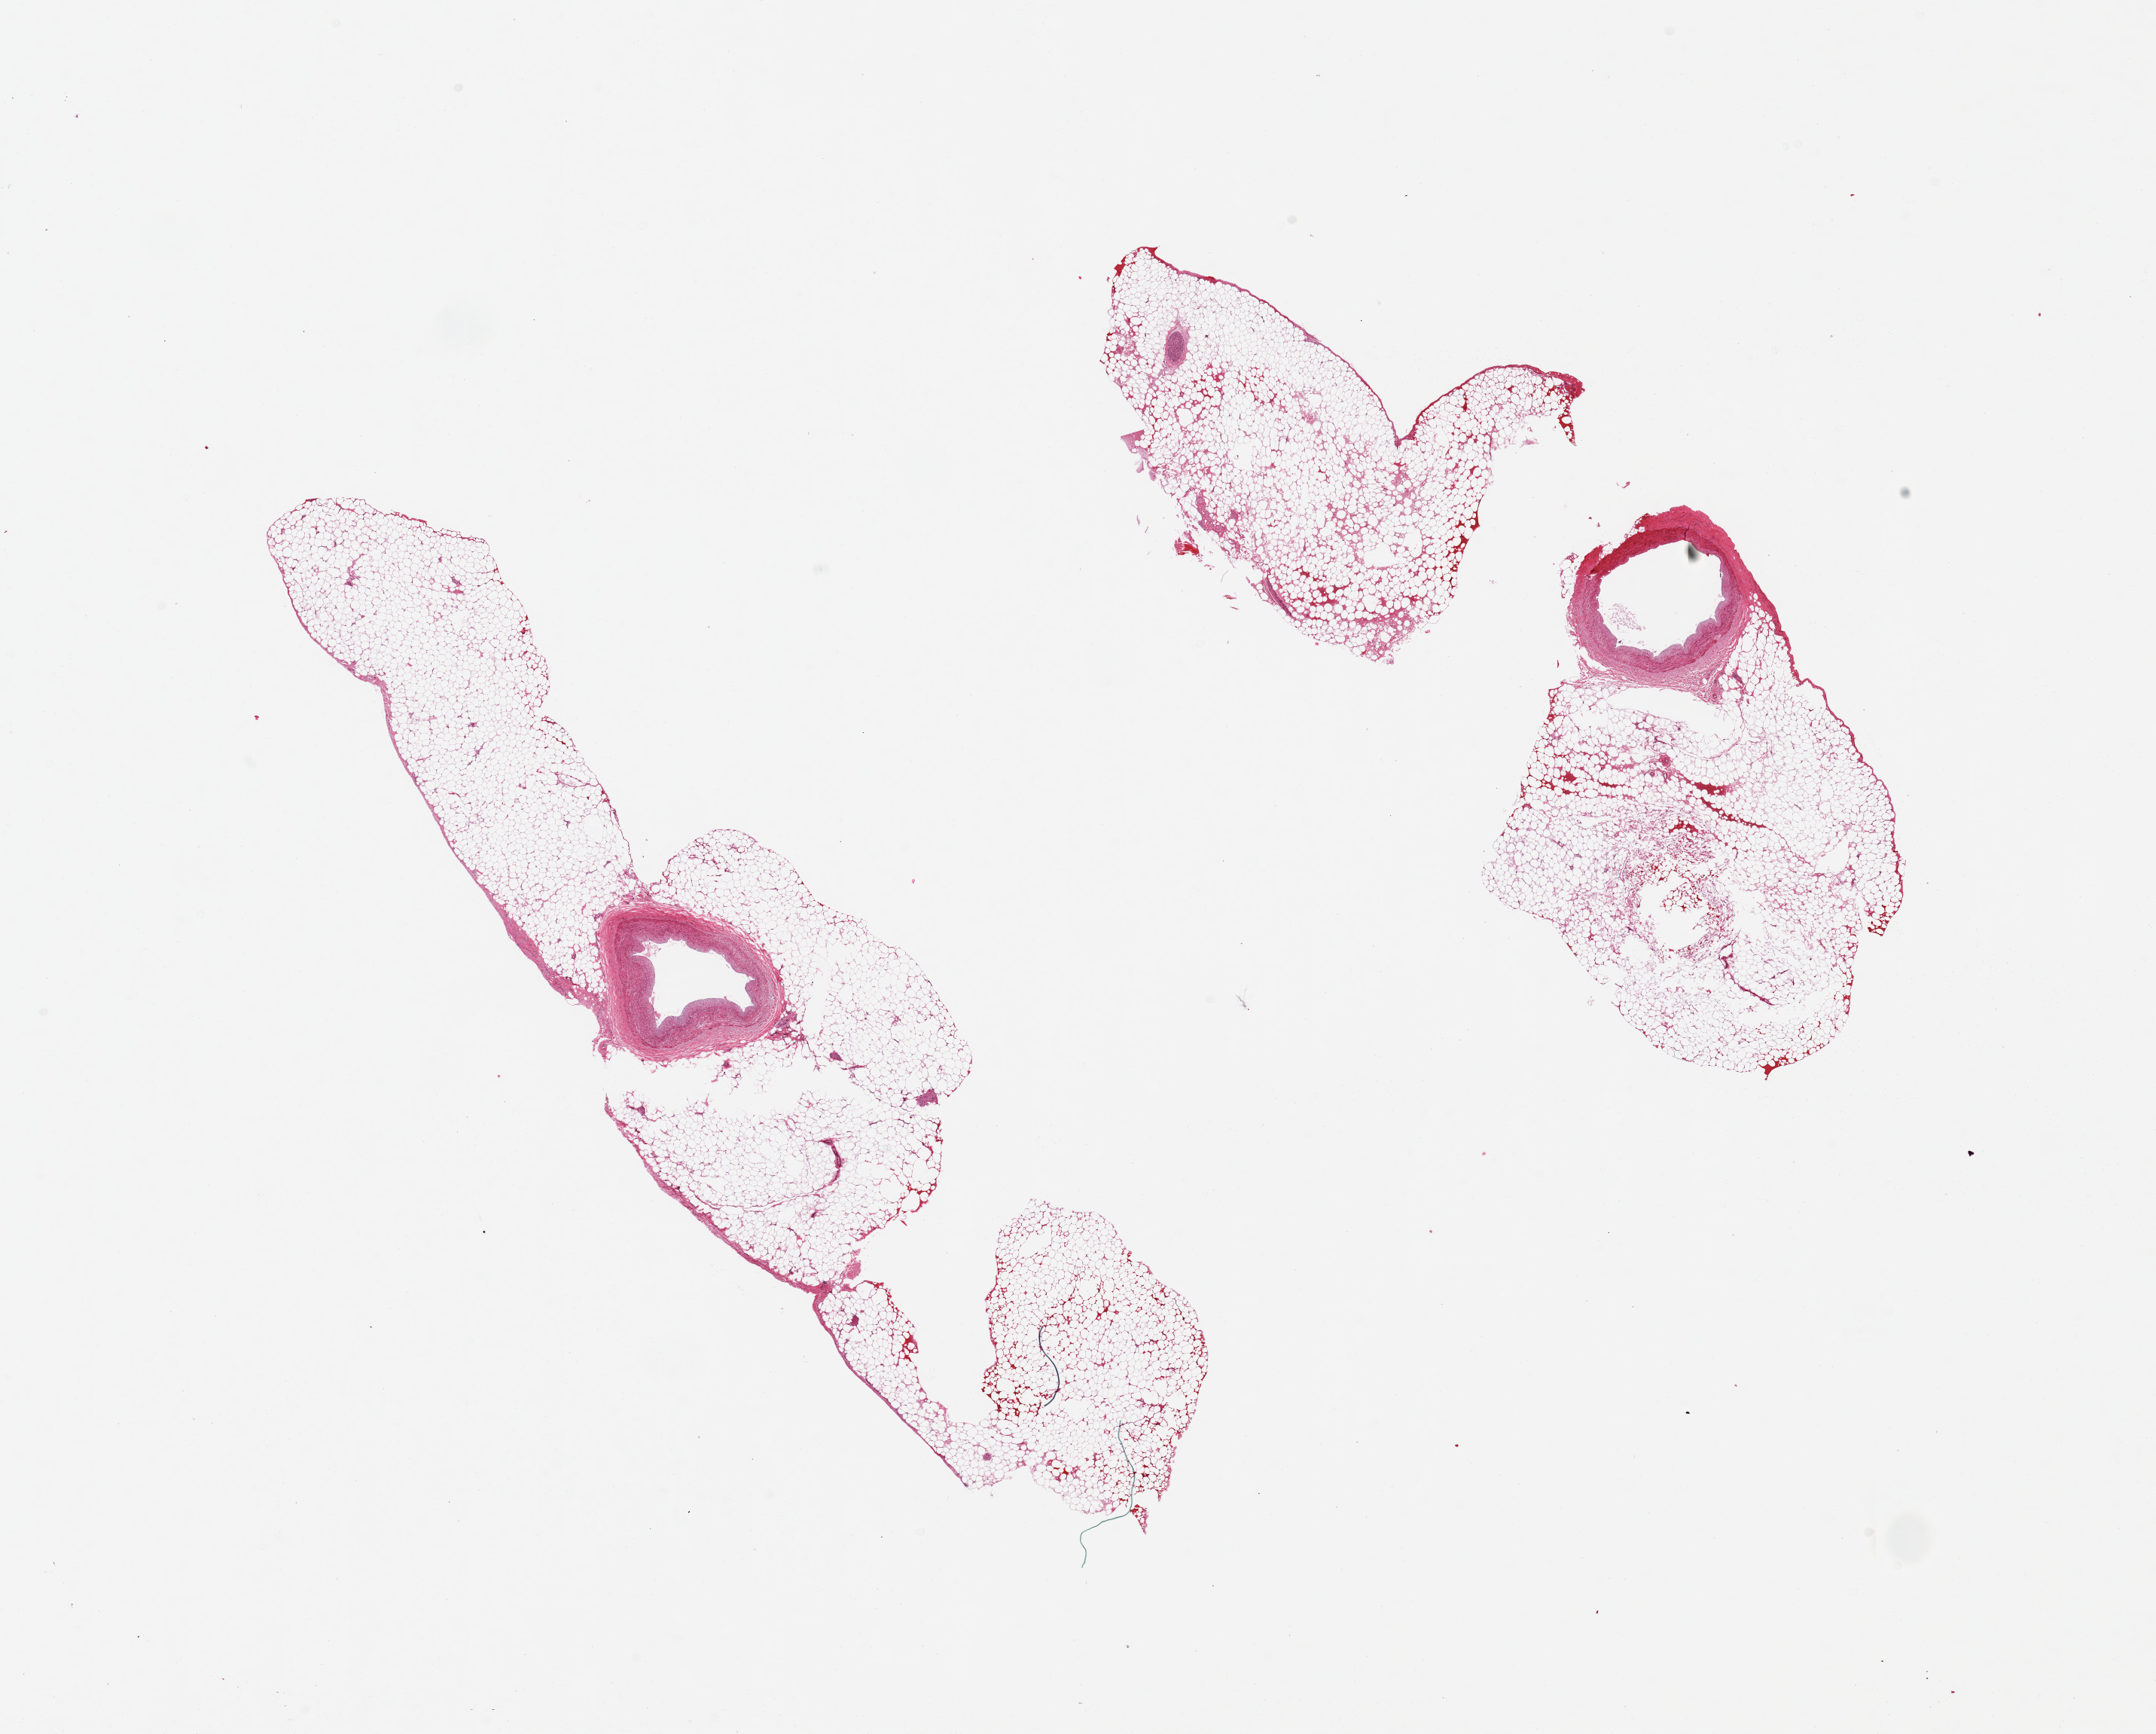
Haematoxylin and eosin whole-slide image — shown as a low-resolution overview of the whole scanned area (about 22.6 x 18.2 mm). PAXgene-fixed paraffin-embedded (PFPE) section. Target tissue: coronary artery. Donor tissue sample.
Pathologist's review note for this sample: 2 pieces, minute vessel, possible branch of LCA, mainly pericardial fat.